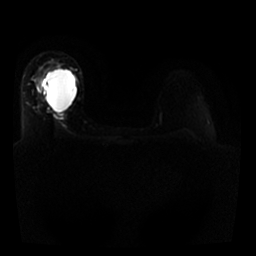
Breast MRI, one axial slice. Position 18 of 25 along the scan axis. Diffusion-weighted series; image 2 of 4 stored at this slice position (different b-values; order by instance number). 1.5 T. 4 mm slice thickness. 256 × 256 image matrix. Female patient.
Structures marked on this image (outlined manually by an expert reader):
- tumour on diffusion-weighted imaging: bounding box (x1, y1, x2, y2) in pixels: (39, 75, 45, 91)